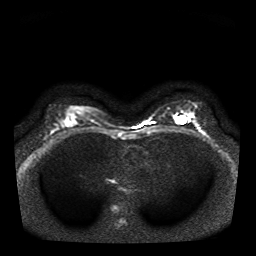
Breast MRI, one axial slice. Slice 22 of 41 in the series (ordered by position). Diffusion-weighted series; image 2 of 4 stored at this slice position (different b-values; order by instance number). 1.5 T. 5 mm slice thickness. 256 × 256 image matrix, field of view 330 × 330 mm. Female patient.
Structures marked on this image (outlined manually by an expert reader):
- tumour on diffusion-weighted imaging: bounding box (x1, y1, x2, y2) in pixels: (188, 114, 194, 122)